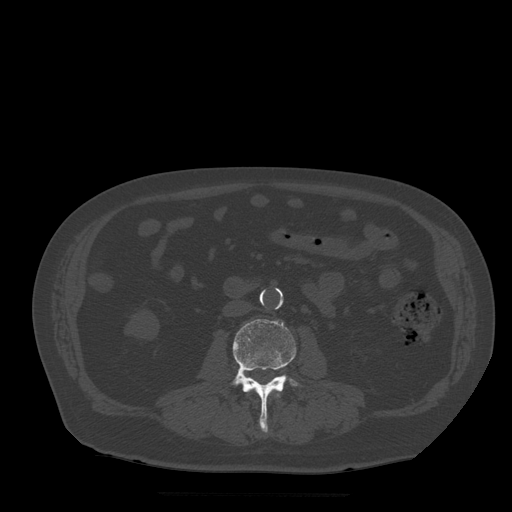
CT including the spine, one axial slice; bone window (W 1800 / L 400 HU); 1.25 mm slice thickness; 512 × 512 image matrix, field of view 420 × 420 mm. Patient age 72 years. From the clinical record (not read from this slice): primary cancer: prostate.
Outlined on this slice (semi-automatic segmentation, software-assisted and operator-edited):
- L2 vertebra: bounding box [x1, y1, x2, y2] px = [248, 392, 280, 398]
- L3 vertebra: [231, 320, 302, 432]